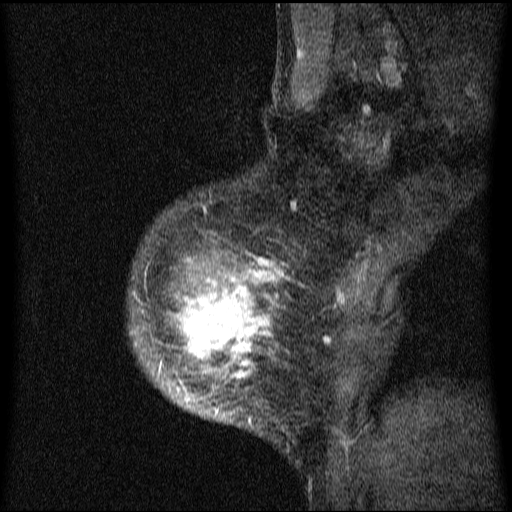
Breast MRI (dynamic contrast-enhanced), one sagittal slice; position 53 of 64 along the scan axis; dynamic contrast-enhanced series, image 2 of 4 at this slice position (ordered by acquisition); 1.5 T; TE 4.2 ms, TR 9.1 ms; 2 mm slice thickness; 512 × 512 image matrix. Patient: female, 33 years.
Annotated regions visible in this slice (semi-automatically segmented with operator editing):
- analysis volume of interest (the breast-tissue region the enhancement analysis was run in; not a lesion): bounding box (x1, y1, x2, y2) in pixels: (130, 151, 335, 450)
- tumour enhancement mask (voxels above the 70 % enhancement threshold inside the analysis volume of interest): (132, 258, 331, 425)